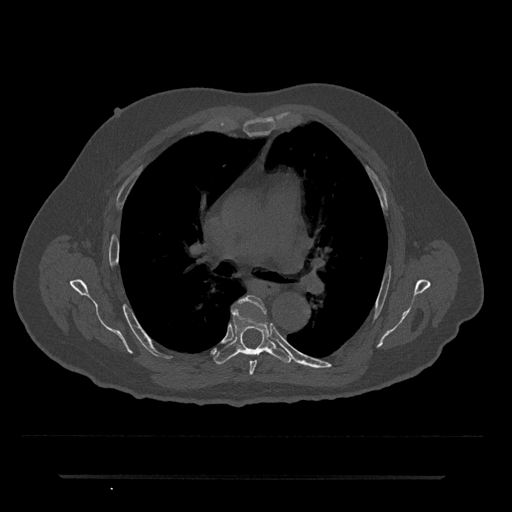
CT including the spine, one axial slice. Slice 452 of 797 in the series (ordered by position). Reconstruction kernel Br40s/3. 120 kVp. Bone window (W 1800 / L 400 HU). 512 × 512 image matrix. Male patient, age 69 years. Case-level facts recorded for this patient, not image findings: primary cancer: prostate.
Outlined on this slice (semi-automatic segmentation, software-assisted and operator-edited):
- T5 vertebra: bounding box <233,296,266,375> (left, top, right, bottom; pixels)
- T6 vertebra: <214,308,292,364>